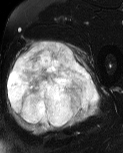
MRI of an extremity soft-tissue mass, one axial slice; T2-weighted fat-saturated; MR volume resampled by the dataset authors to the PET/CT grid (not the native acquisition matrix); 3.27 mm slice thickness; 123 × 153 image matrix, field of view 120 × 149 mm. Male patient. From the clinical record (not read from this slice): histological type: pleiomorphic liposarcoma; grade: high; site of the primary tumour: left thigh.
Structures marked on this image (expert contour drawn on MRI and transferred to this co-registered scan by the dataset authors):
- gross tumour volume including surrounding oedema: bounding box [x1, y1, x2, y2] px = [6, 40, 101, 135]
- gross tumour volume (mass): [8, 42, 99, 128]